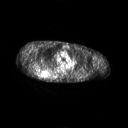
FDG PET of an extremity soft-tissue mass (from a PET/CT study), one axial slice. Slice 183 of 267 in the series (ordered by position). 128 × 128 image matrix, field of view 700 × 700 mm. Male patient, age 61 years. Case-level facts recorded for this patient, not image findings: histological type: pleiomorphic spindle cell undifferentiated; grade: high; site of the primary tumour: right parascapusular.
Annotated regions visible in this slice (expert contour drawn on MRI and transferred to this co-registered scan by the dataset authors):
- gross tumour volume including surrounding oedema: box from (x=33, y=69) to (x=57, y=79) px
- gross tumour volume (mass): (x=36, y=69)–(x=49, y=77)